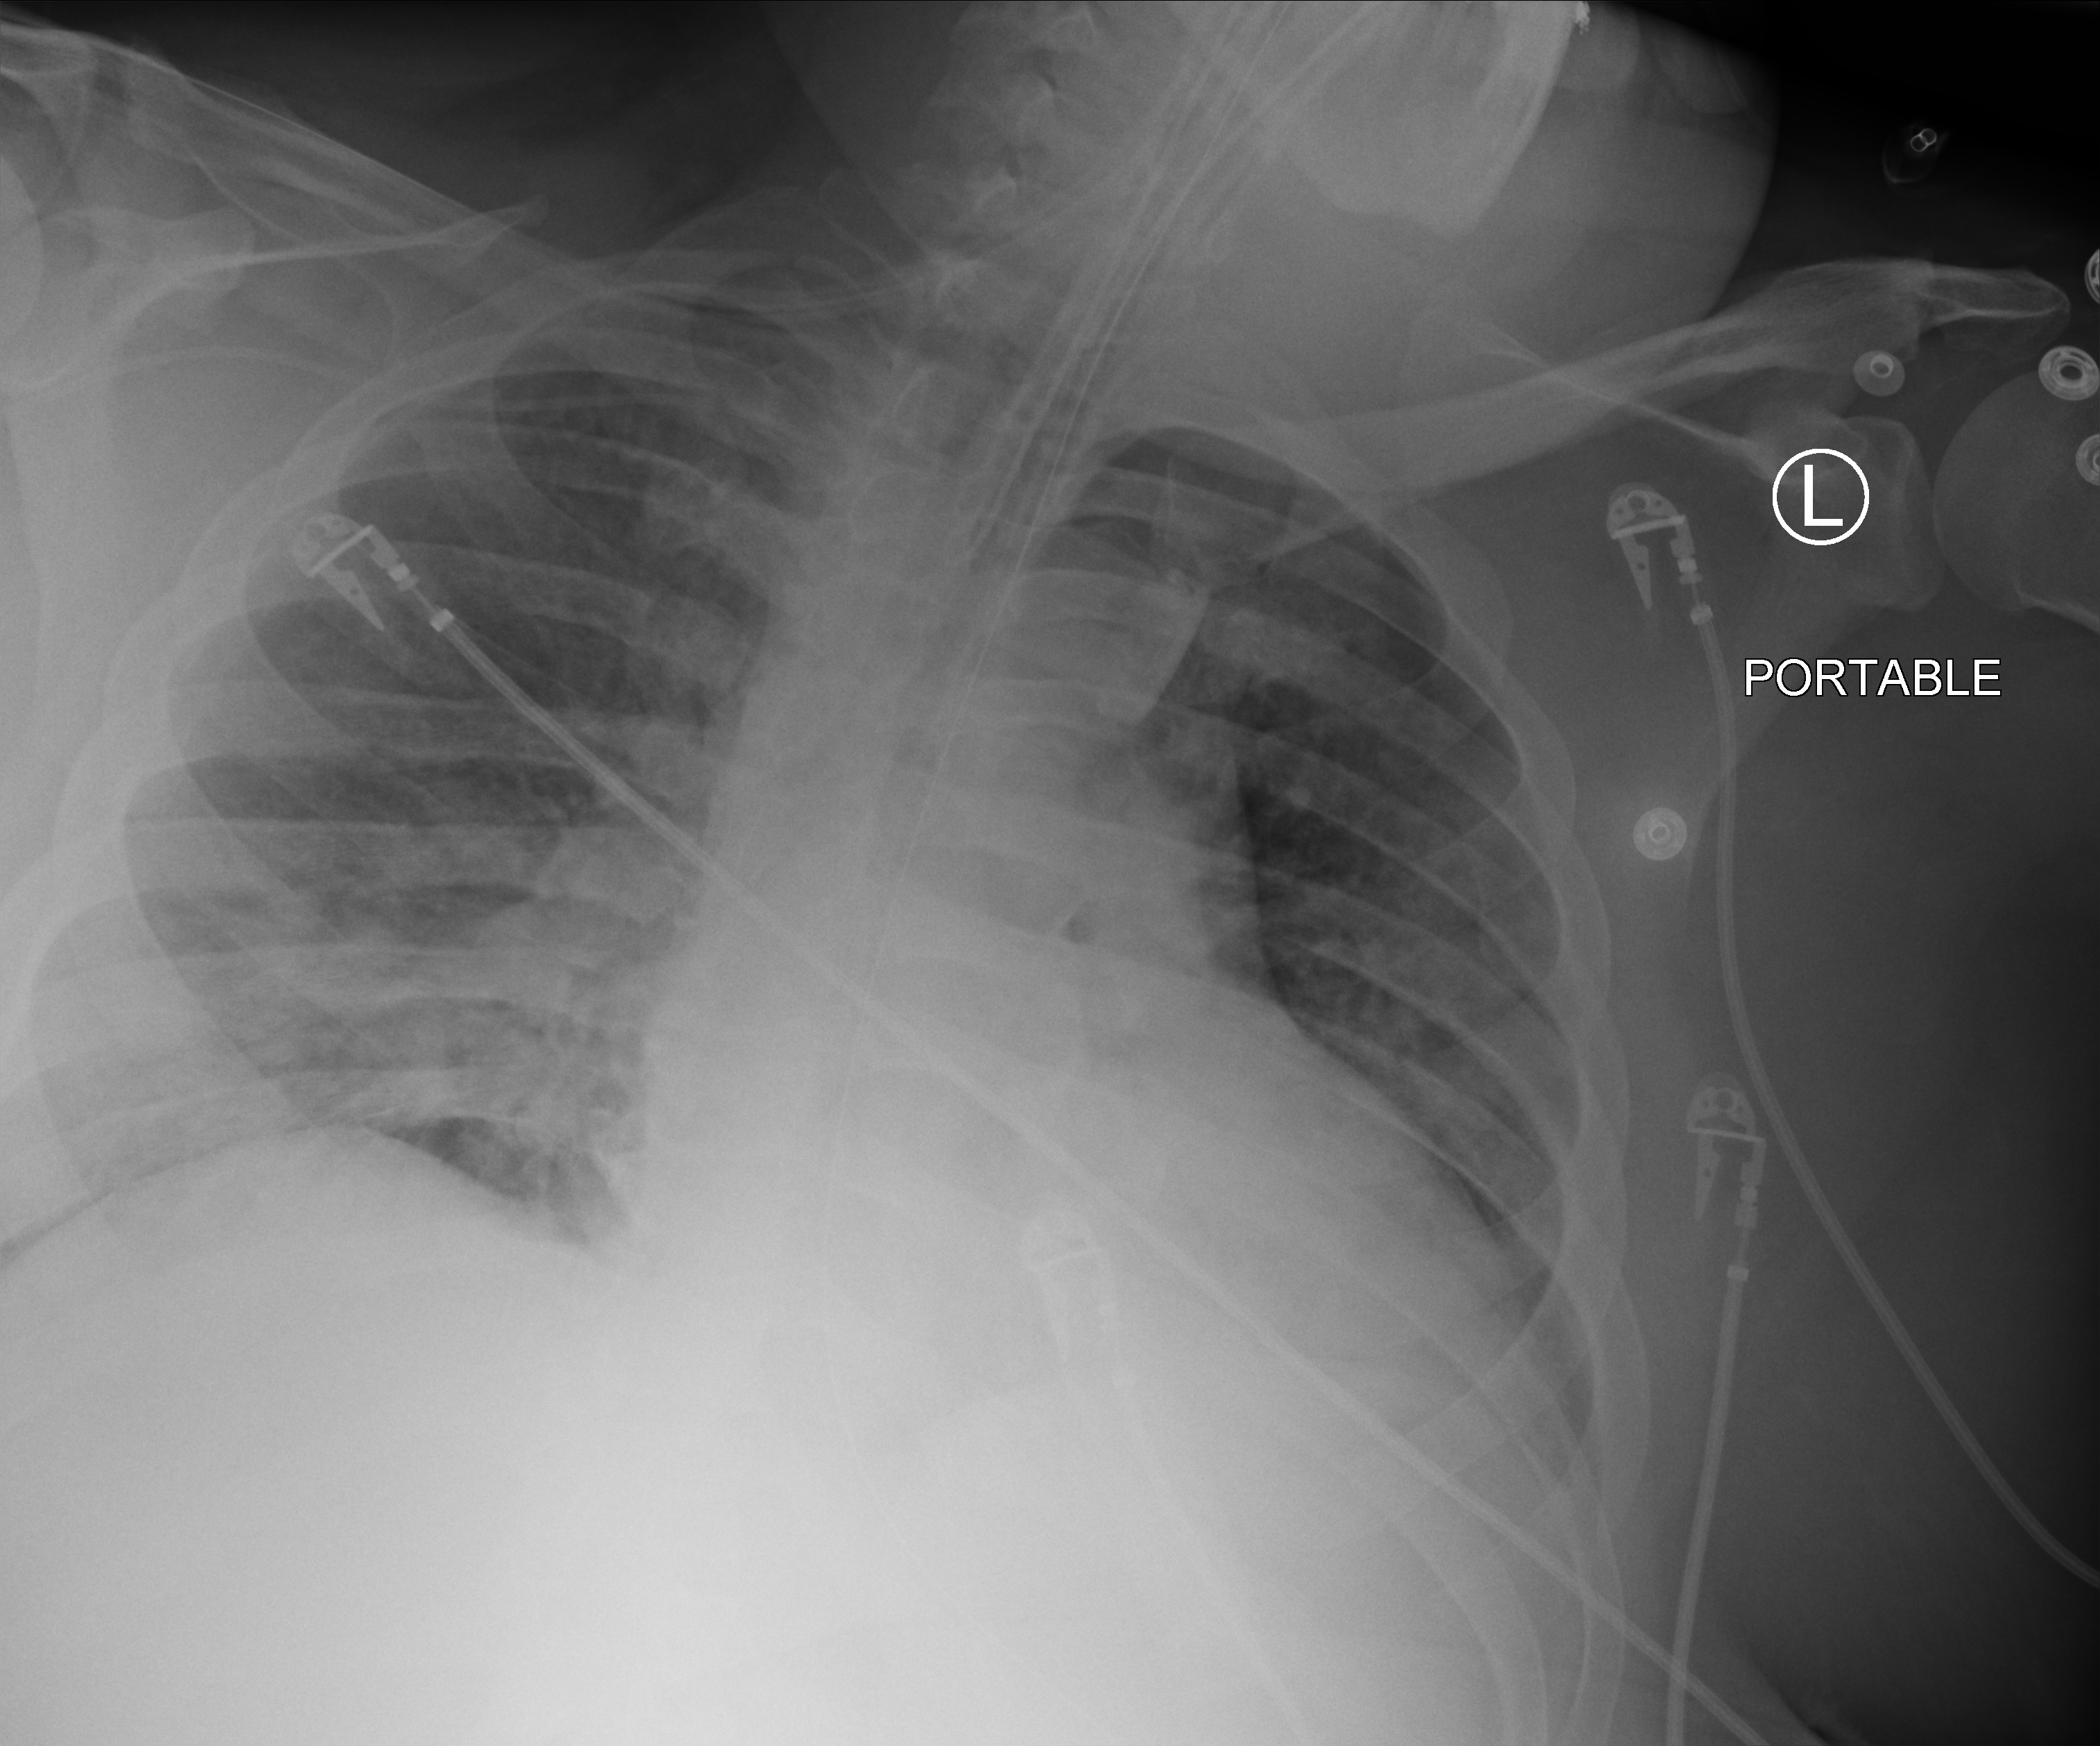
Bedside chest radiograph (computed radiography); anteroposterior (AP) projection. Adult patient hospitalised with COVID-19, age 18–59 years.
Admission-level facts for this patient (not findings on this image; timing relative to this image not recorded): mechanically ventilated during this hospital stay: yes; diabetes (admission record): yes.